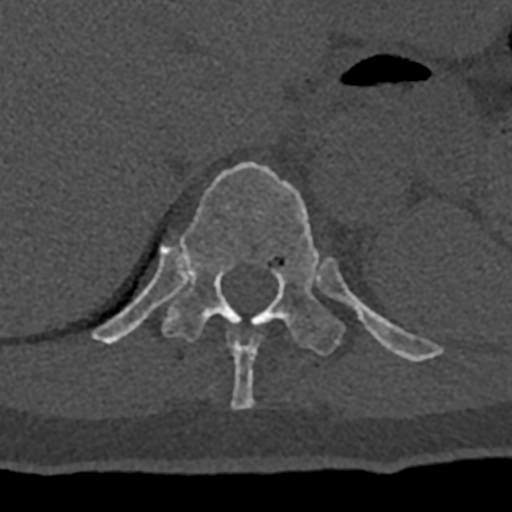
CT including the spine, one axial slice. Position 562 of 797 along the scan axis. Reconstruction kernel Br40s/3. 120 kVp. Bone window (W 1800 / L 400 HU). 0.5 mm slice thickness. 512 × 512 image matrix, field of view 160 × 160 mm. Male patient, age 74 years. From the clinical record (not read from this slice): primary cancer: renal; vertebrae with lytic lesions (as recorded): T10, L1, L2, L3, L4, L5.
Structures marked on this image (semi-automatically segmented with operator editing):
- T10 vertebra: bounding box (x1, y1, x2, y2) in pixels: (226, 330, 263, 409)
- T11 vertebra: (92, 162, 432, 361)